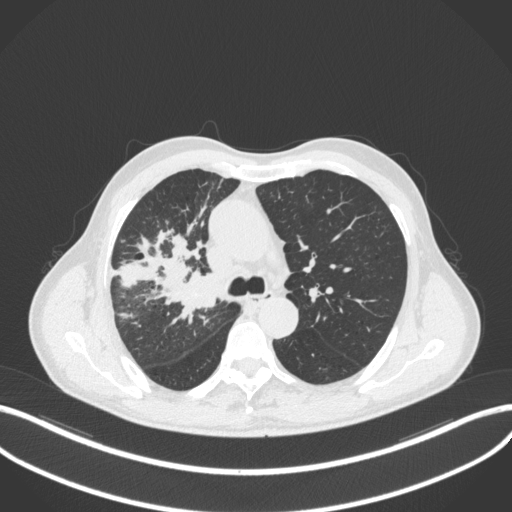
Chest CT, one axial slice; position 327 of 490 along the scan axis; reconstruction kernel B31f; 120 kVp; lung window (W 1500 / L -600 HU); 1 mm slice thickness; 512 × 512 image matrix, field of view 400 × 400 mm. Male patient, age 69 years. Case-level facts recorded for this patient, not image findings: clinical TNM (as recorded): T2a N0 M0.
Annotated regions visible in this slice (bounding box drawn by a radiologist):
- lung tumour (recorded histology: adenocarcinoma): box from (x=181, y=268) to (x=219, y=314) px